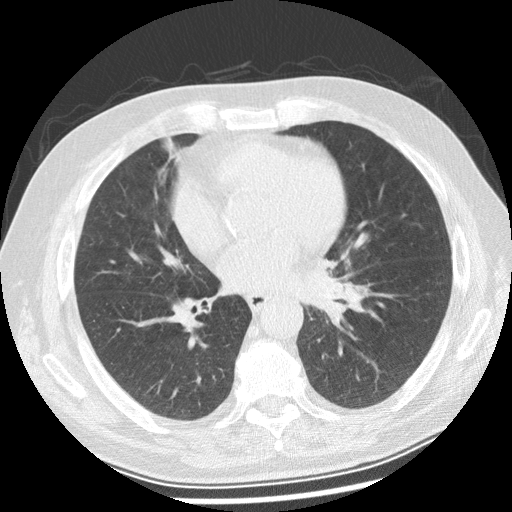
Low-dose screening chest CT, one axial slice; position 122 of 250 along the scan axis; reconstruction kernel STANDARD; 120 kVp; lung window (W 1500 / L -600 HU); 2.5 mm slice thickness; 512 × 512 image matrix, field of view 360 × 360 mm.
Structures marked on this image (manually delineated by an expert):
- lesion 1 (tumor, left main bronchus): bounding box (x1, y1, x2, y2) in pixels: (323, 258, 338, 274)